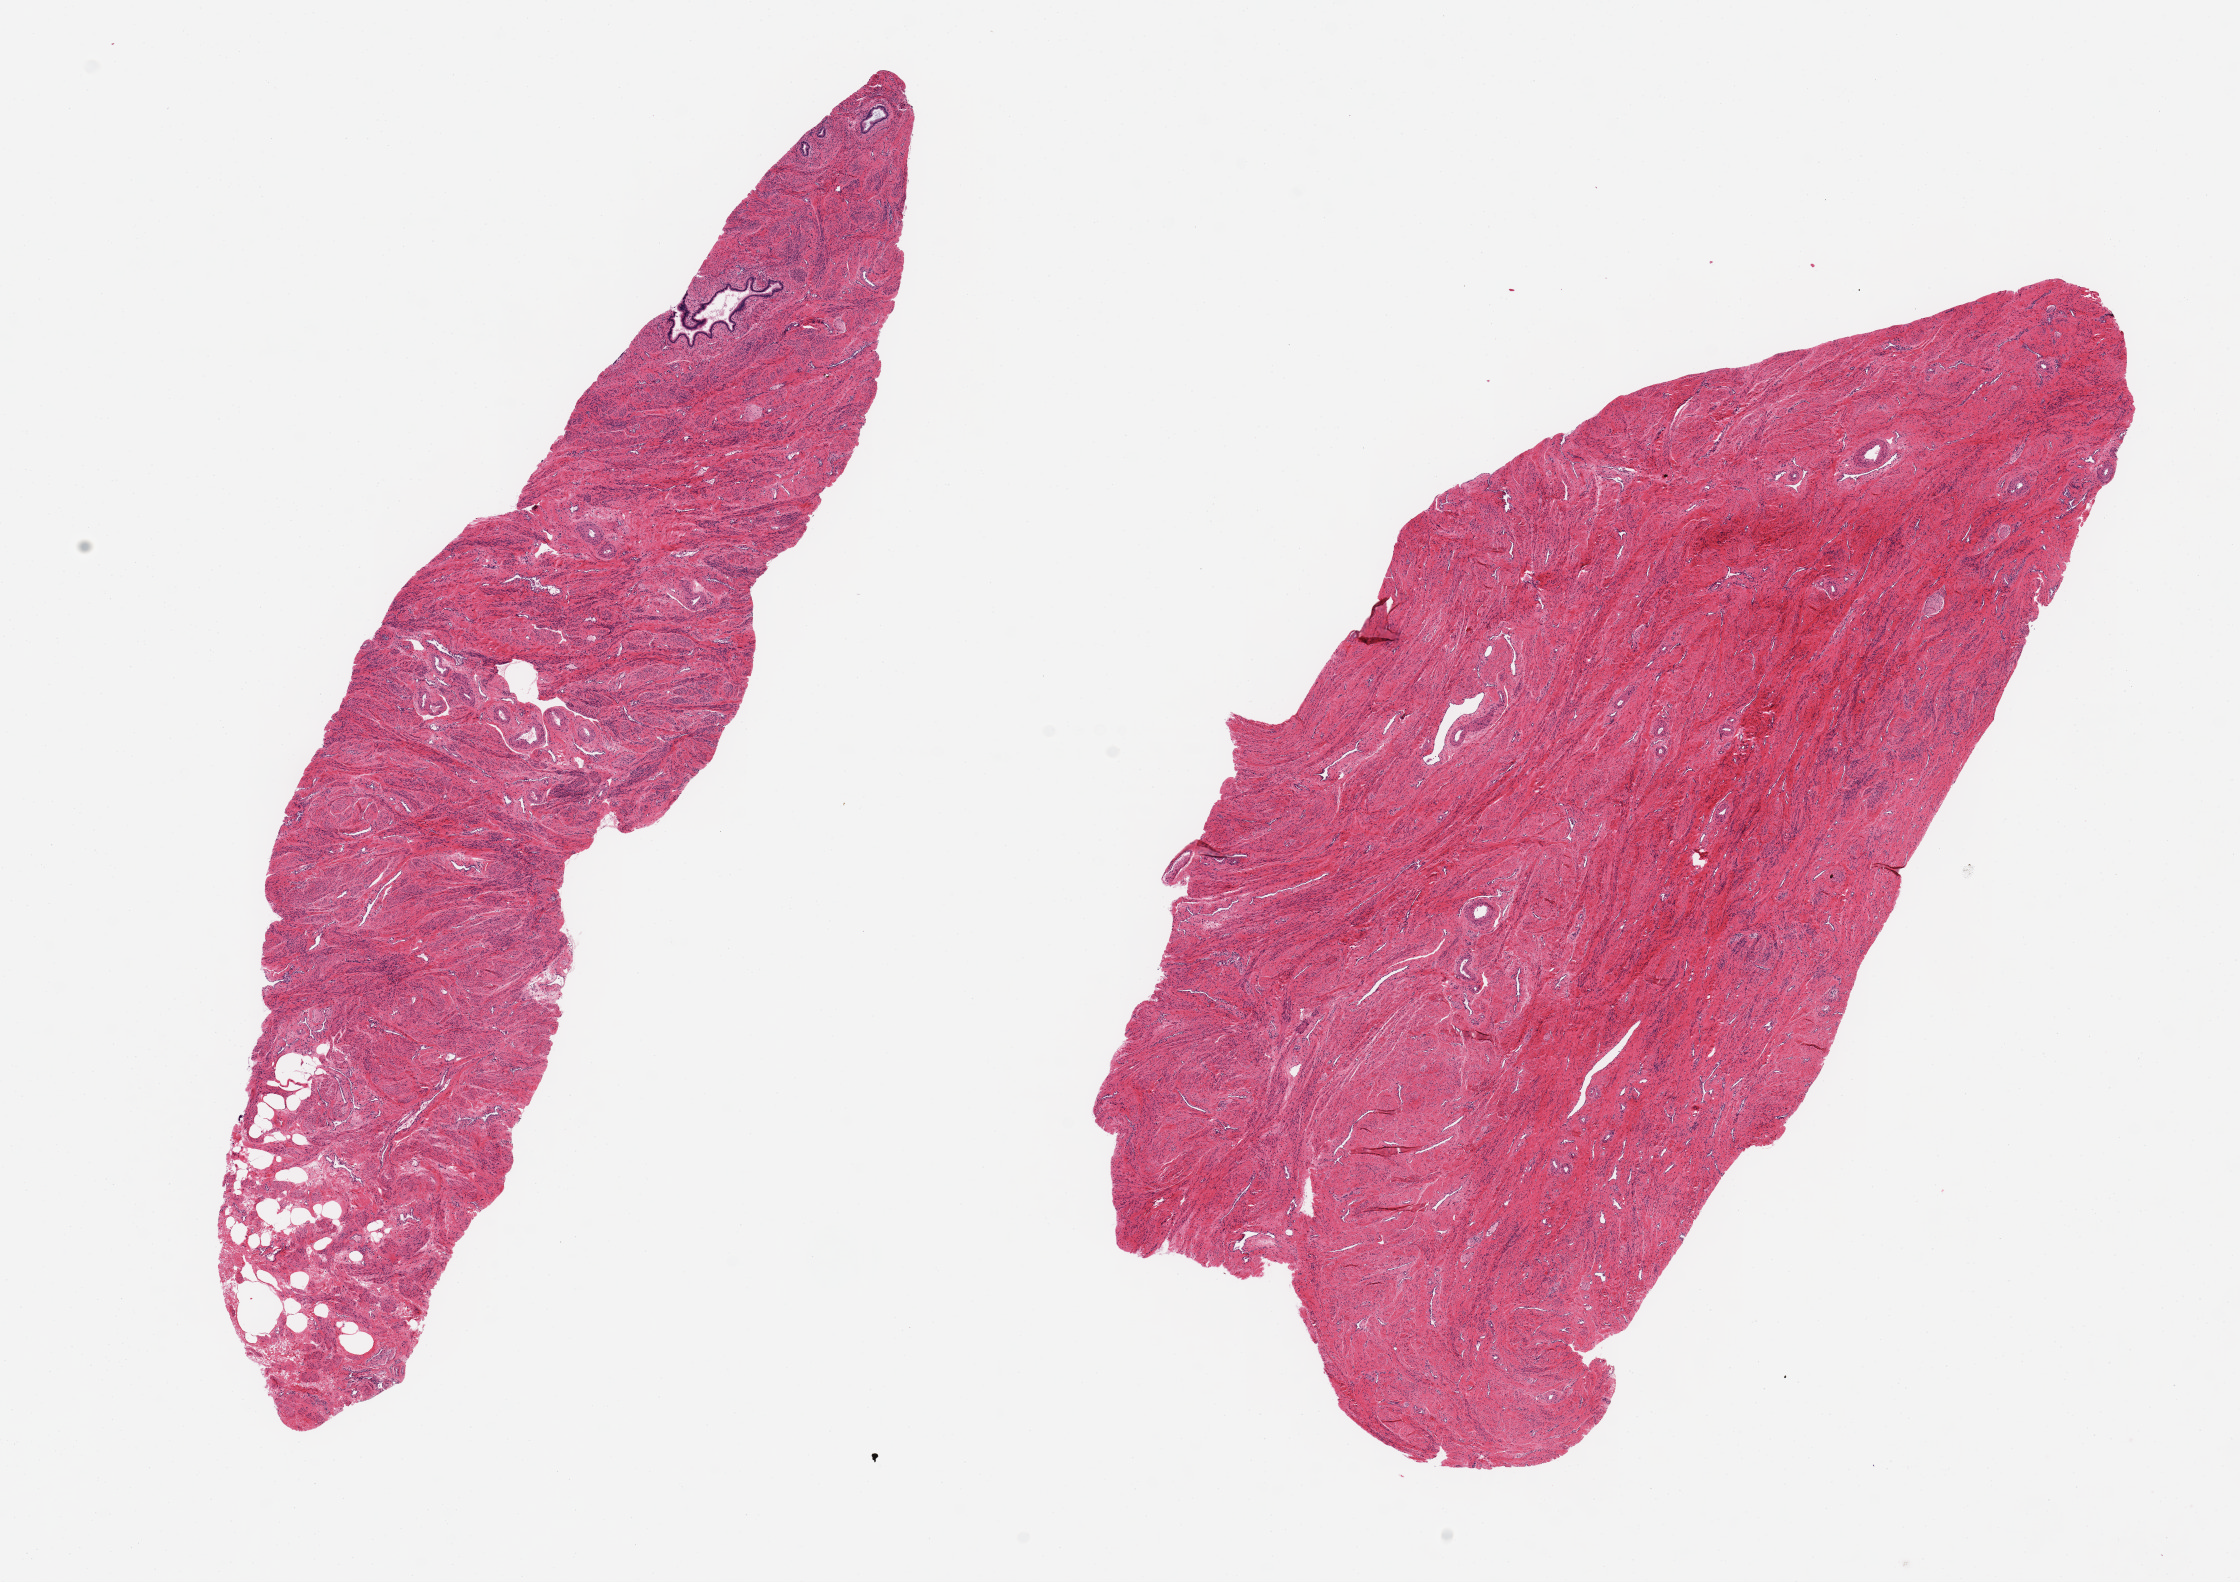
Haematoxylin and eosin whole-slide image — a low-resolution overview of the entire scanned area, about 17.7 x 12.5 mm. PAXgene-fixed paraffin-embedded (PFPE) section. Target tissue: uterus. Donor tissue sample. Donor sex: female.
Reviewer comment on this tissue sample: 2 ~10x4mm aliquots. 99% myometrium; rare focal glands, probably lower uterine segment/upper endocervix.